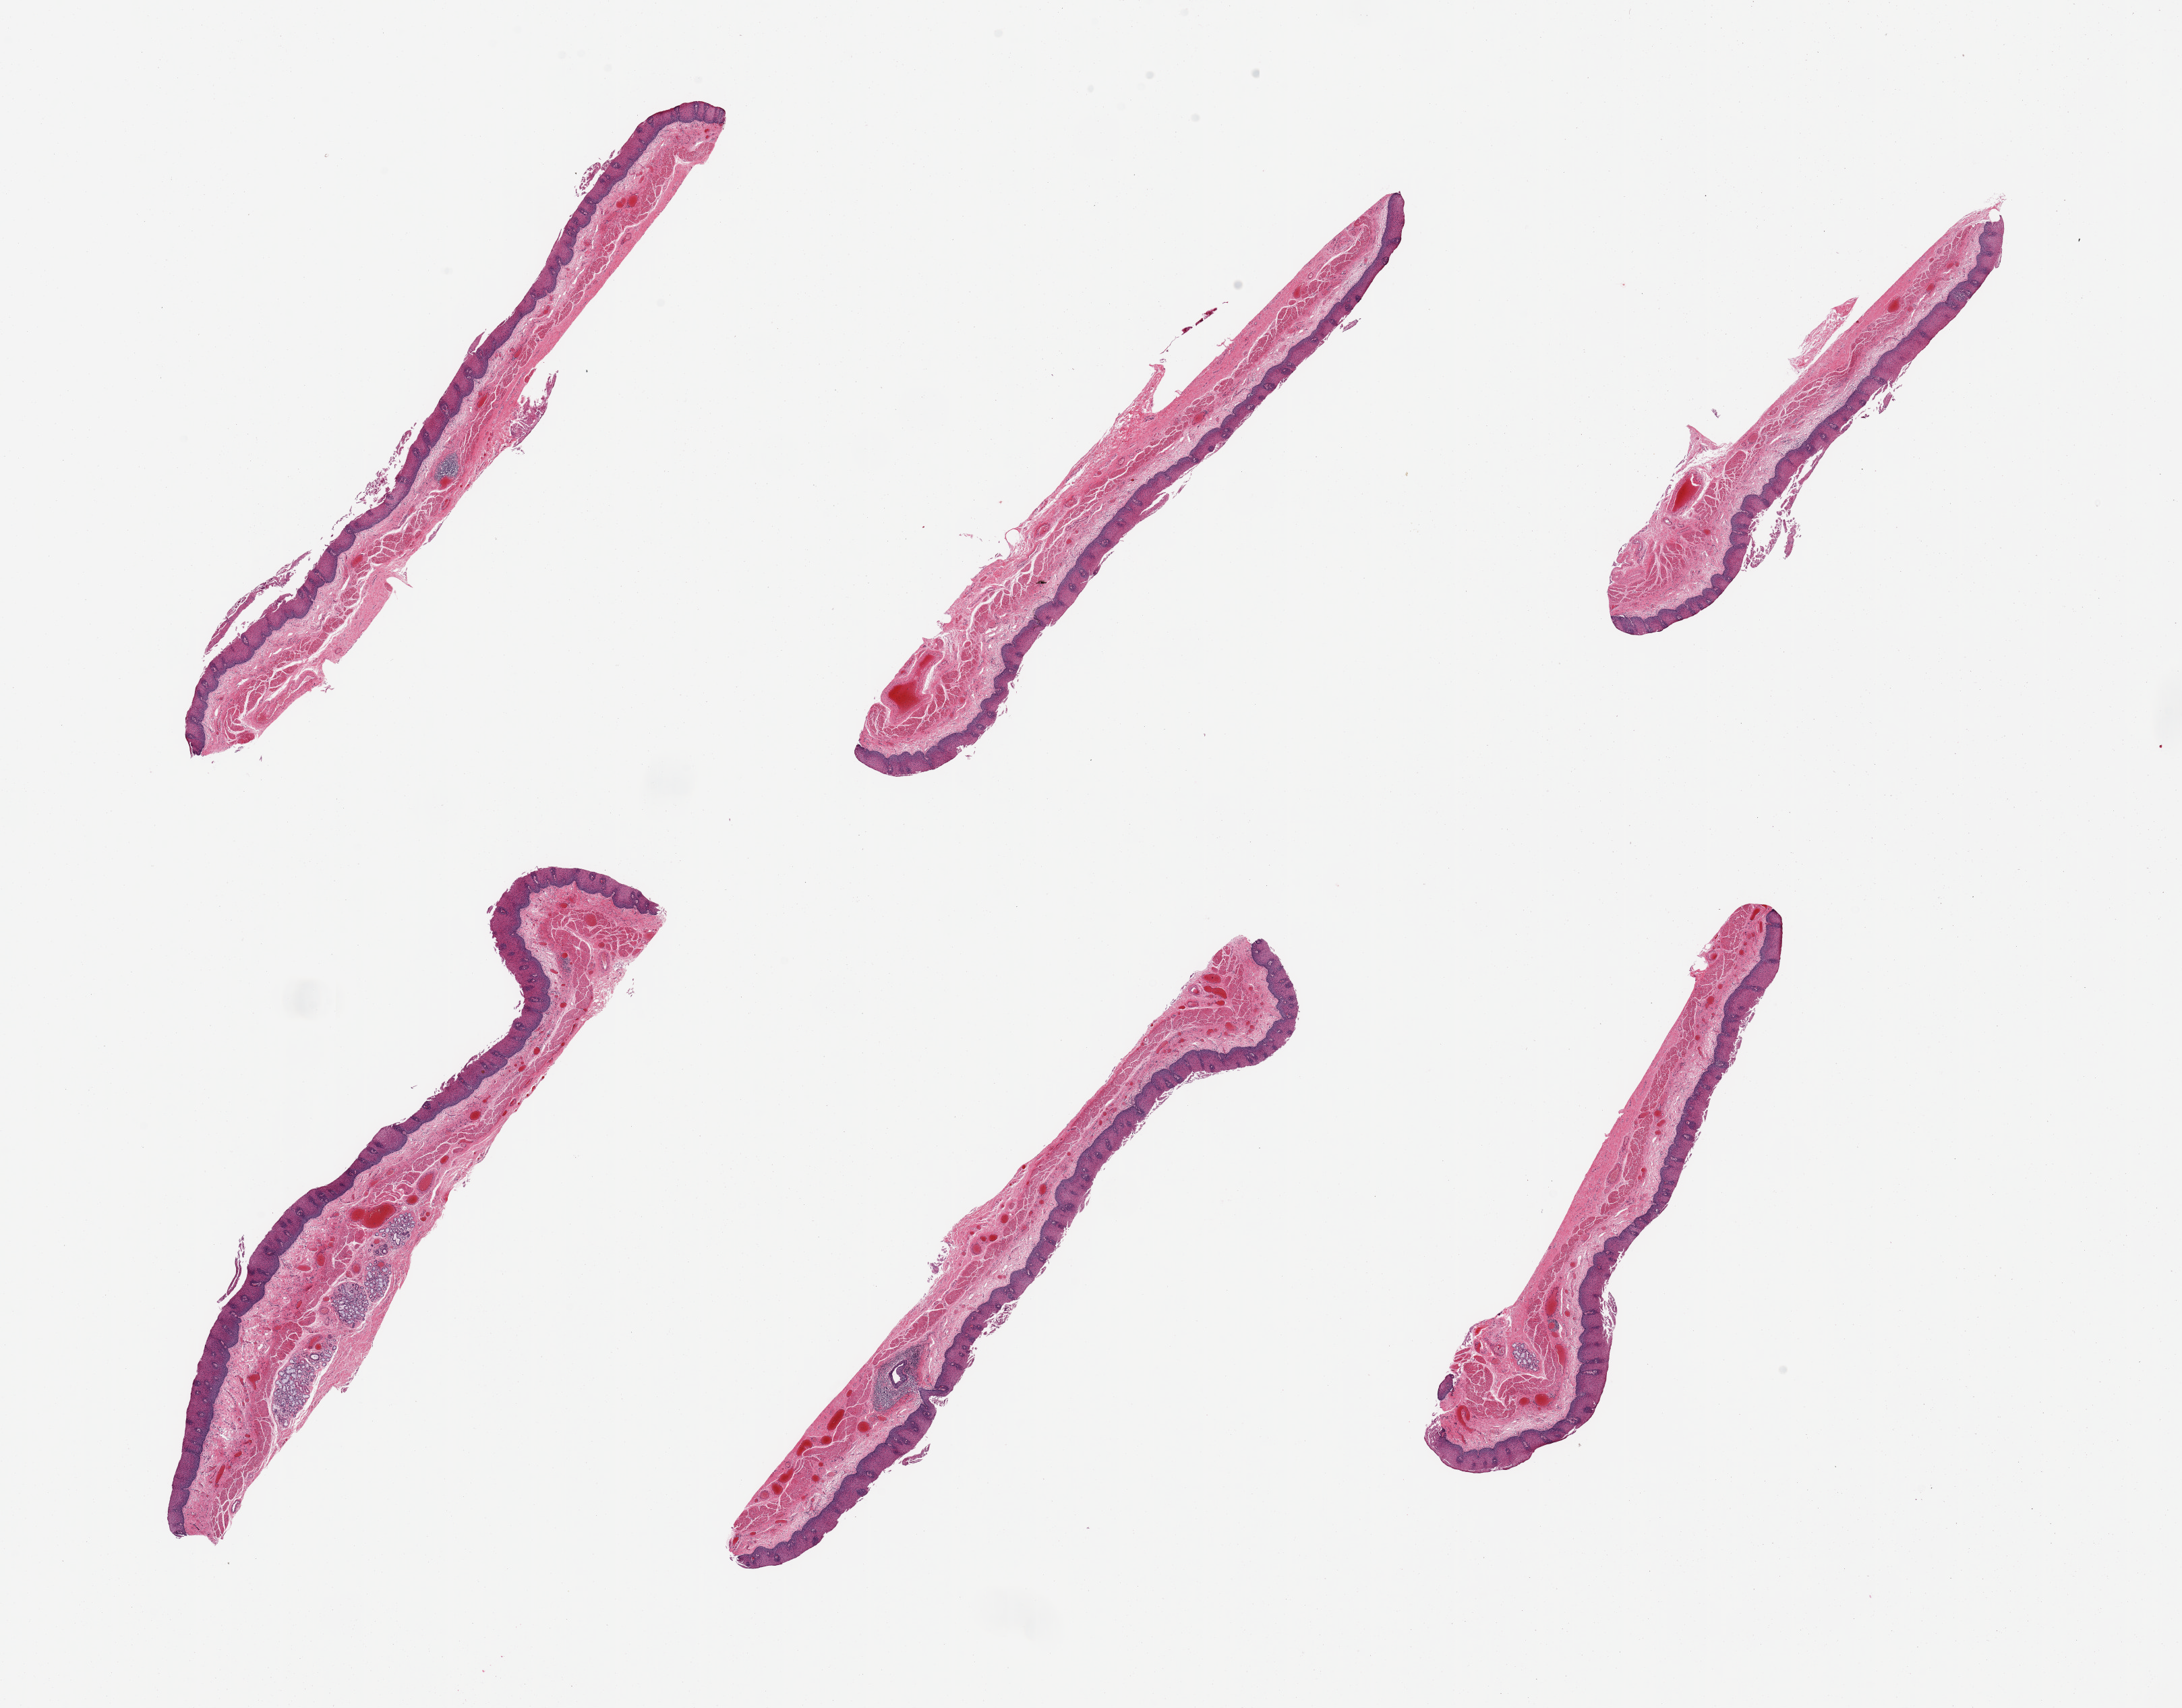
Haematoxylin and eosin whole-slide image, brightfield, whole scanned area (about 25.6 x 20.0 mm, slide scanned at 20x) shown as a low-resolution overview. PAXgene-fixed paraffin-embedded (PFPE) section. Sampled site (target tissue): esophageal mucous membrane. Donor tissue sample. Male donor.
- pathologist's review note for this sample: 6 pieces; small foci of chronic inflammation